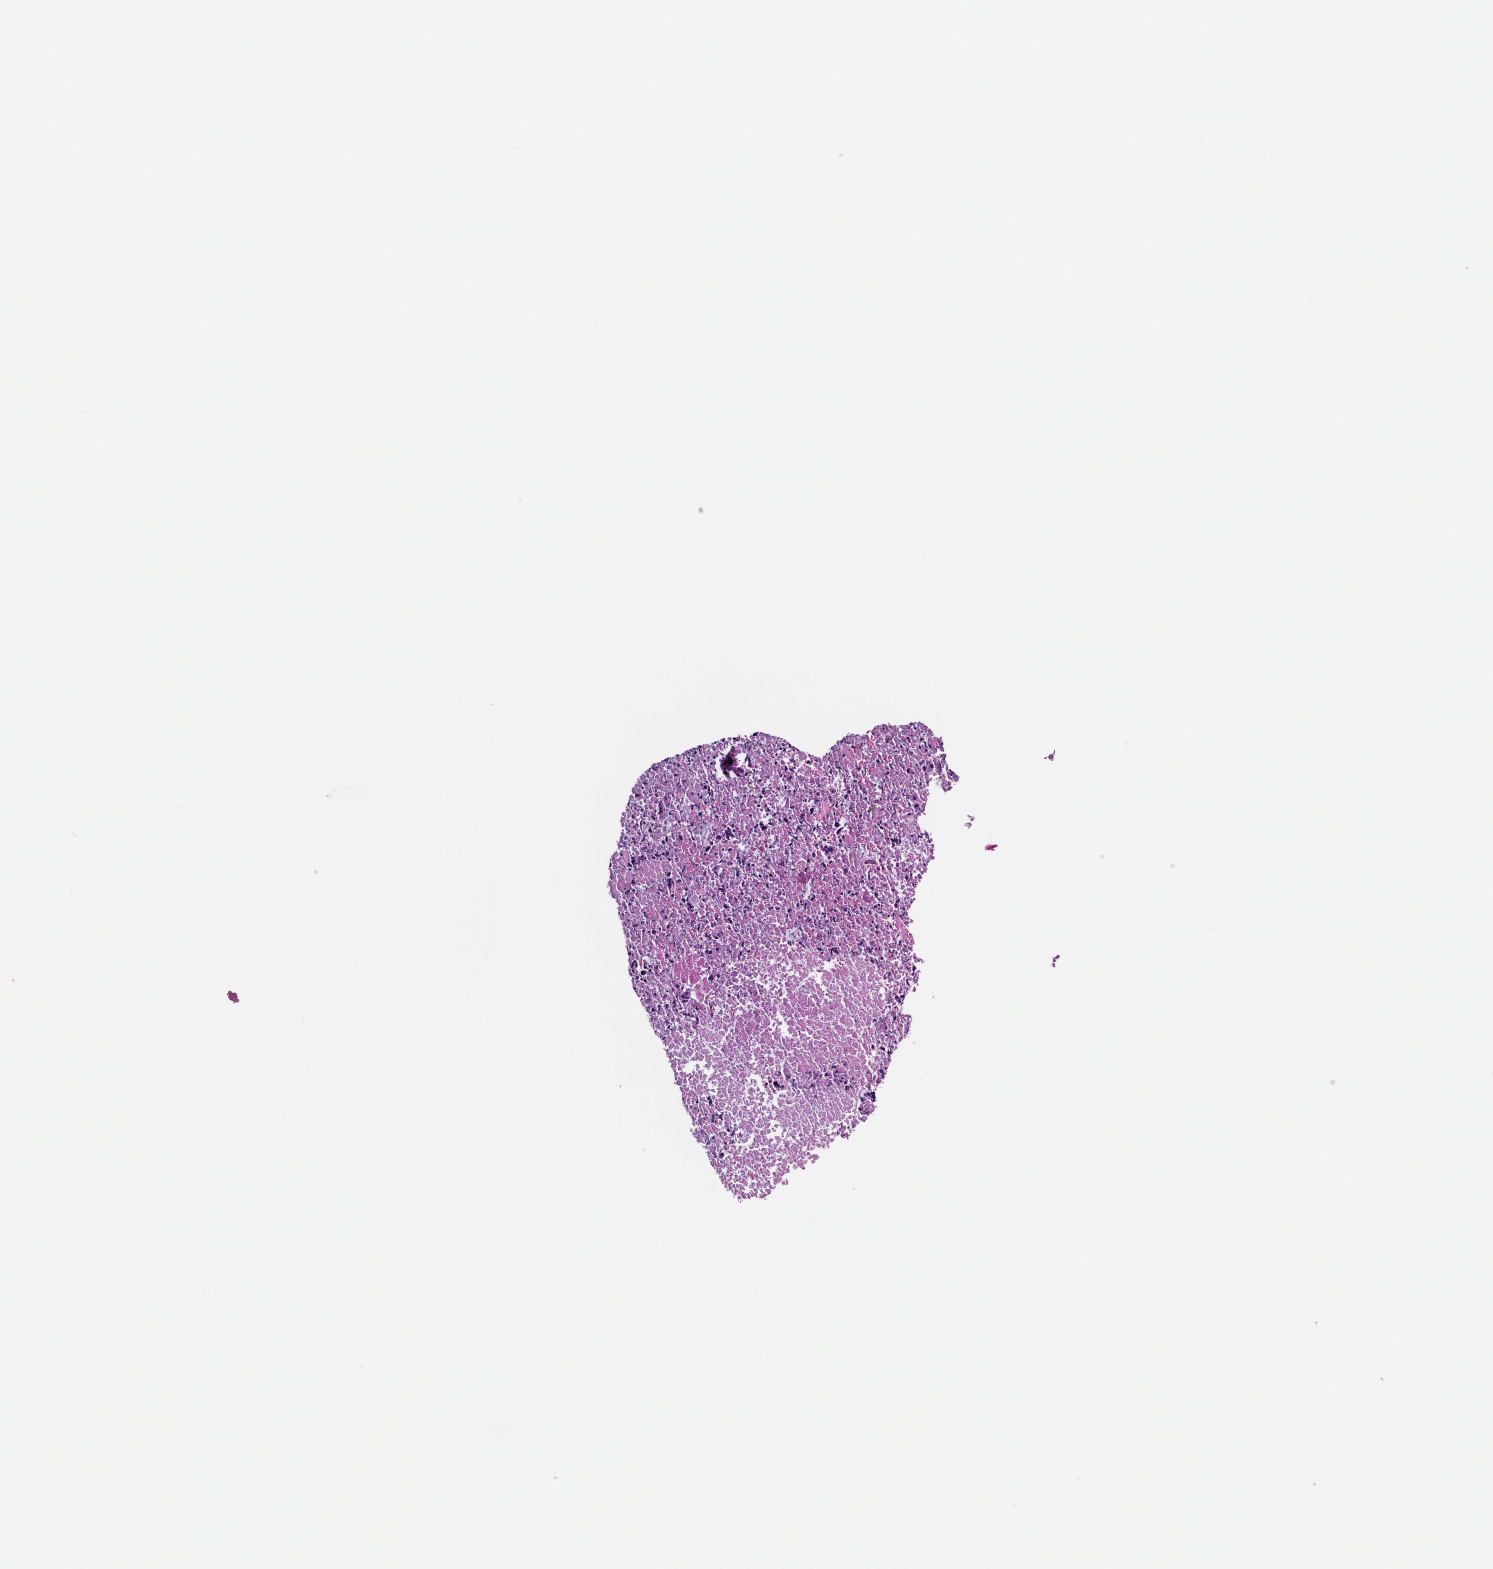
Digitized H&E-stained section, whole scanned area (about 3.0 x 3.2 mm) shown as a low-resolution overview; FFPE section; specimen time point: archival tissue. Male patient.
This section: metastasis (sampled organ not recorded). Primary diagnosis of the patient: Colorectal Carcinoma.